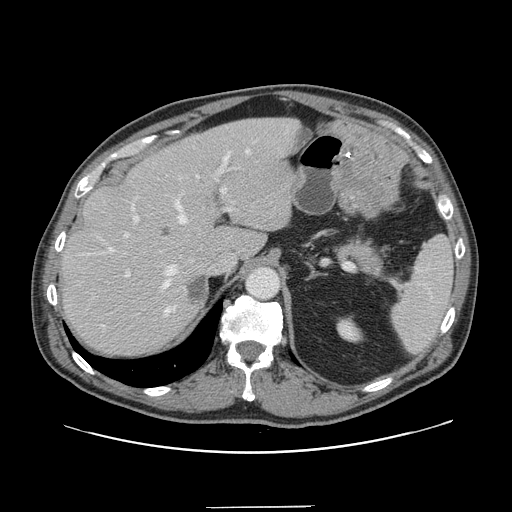
Contrast-enhanced abdominal CT, one axial slice. Position 106 of 139 along the scan axis. Intravenous contrast given. Soft-tissue window (W 400 / L 40 HU). 2.5 mm slice thickness. 512 × 512 image matrix, field of view 397 × 397 mm. Male patient, age 64 years. Case-level facts recorded for this patient, not image findings: diagnosis: colorectal cancer liver metastases, imaged before liver resection; multiple liver metastases: yes; largest metastasis: 3.5 cm; chemotherapy before resection: yes.
Outlined on this slice (manually delineated by an expert):
- hepatic veins: bounding box (x1, y1, x2, y2) in pixels: (108, 149, 250, 315)
- liver: (62, 118, 298, 354)
- planned liver remnant (the part of the liver to remain after resection): (61, 119, 274, 354)
- portal vein (with intrahepatic branches): (124, 151, 232, 277)
- liver metastasis: (187, 276, 206, 304)